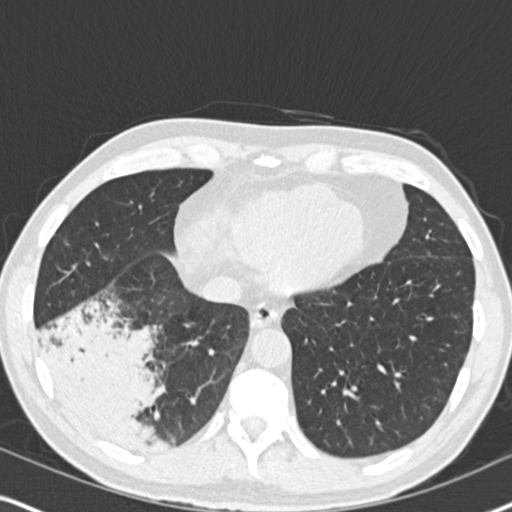
Low-dose screening chest CT, axial slice. Second screening round (one year after baseline). Lung window (W 1500 / L -600 HU). 2 mm slice thickness. Standard (soft-tissue) reconstruction kernel (B30f). 120 kVp. Male participant, aged 61 years at enrolment.
Expert reader's lesion annotation, bounding box <33,300,184,459> (left, top, right, bottom; pixels). Reader record for this screening exam (exam-level; its link to the box is not recorded): non-calcified nodule or mass ≥4 mm, right lower lobe, 90 × 80 mm, soft tissue attenuation, pre-existing on the prior screen: yes; interval growth: yes. Participant outcome: lung cancer diagnosed 20 days after this screen — bronchiolo-alveolar adenocarcinoma, NOS, right lower lobe, moderately differentiated (G2), stage IIIB (AJCC 6th edition), 90 mm at pathology.